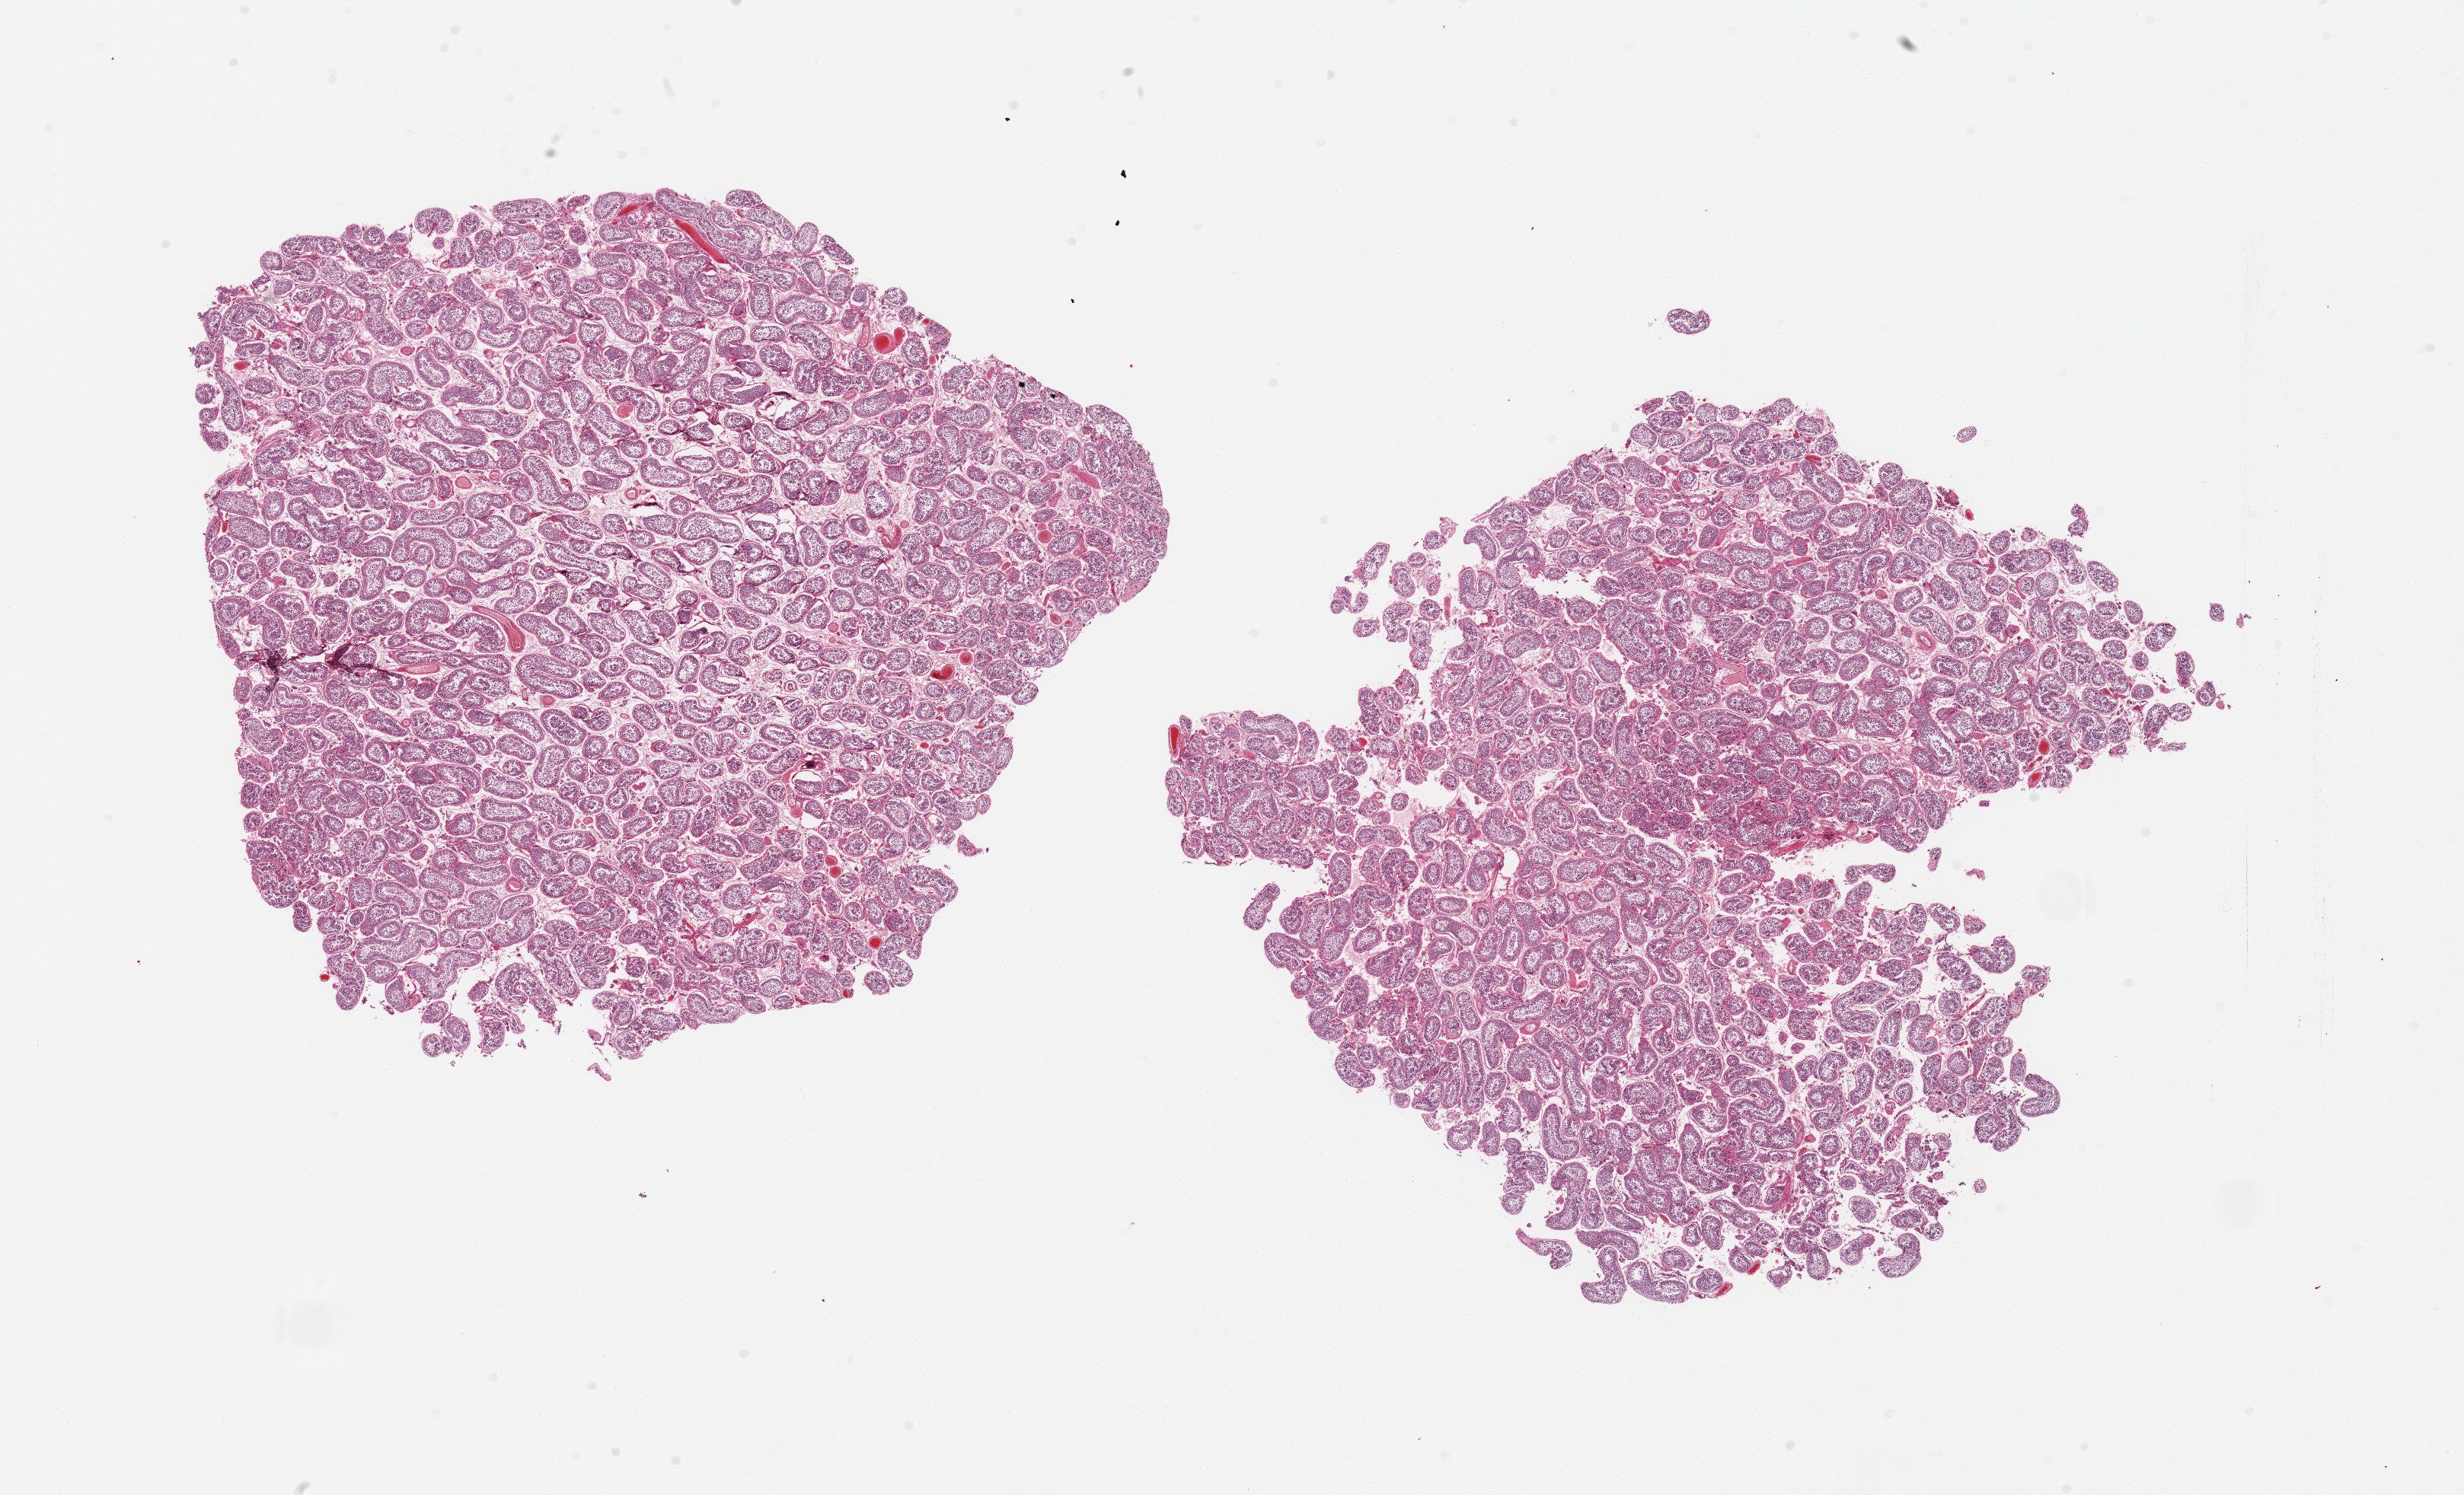
Haematoxylin and eosin whole-slide image, brightfield — shown as a low-resolution overview of the whole scanned area (about 25.6 x 15.5 mm). PAXgene-fixed, paraffin-embedded tissue. Section of testis (target tissue). Donor tissue sample.
* pathologist's review note for this sample: 2 pieces; active spermatogenesis, but poorly preserved